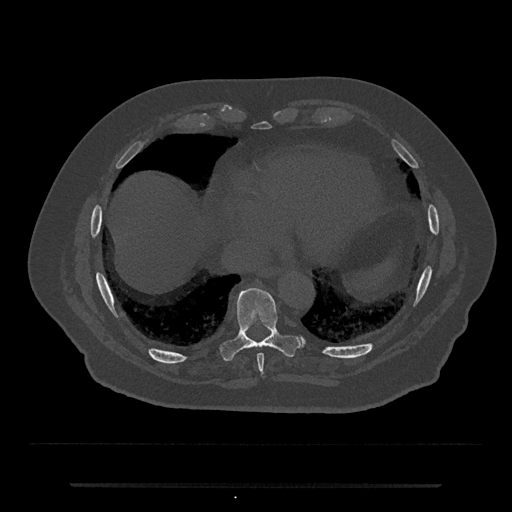
CT including the spine, one axial slice. Position 765 of 797 along the scan axis. Bone window (W 1800 / L 400 HU). 0.5 mm slice thickness. 512 × 512 image matrix, field of view 434 × 434 mm. Male patient, age 80 years. From the clinical record (not read from this slice): primary cancer: prostate.
Structures marked on this image (semi-automatically segmented with operator editing):
- T8 vertebra: bounding box (x1, y1, x2, y2) in pixels: (257, 354, 264, 376)
- T9 vertebra: (221, 285, 303, 361)